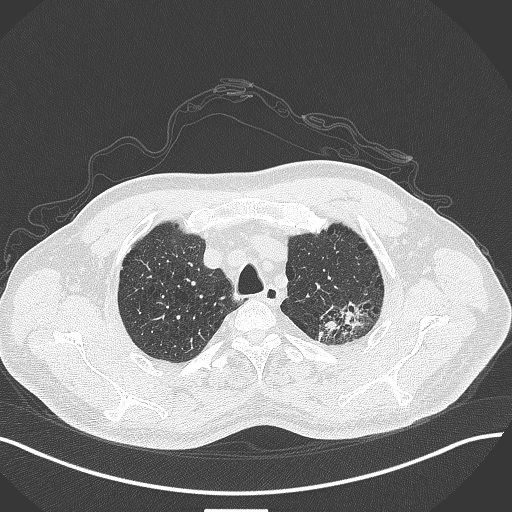
Chest CT, one axial slice. Position 356 of 429 along the scan axis. Reconstruction kernel B70f. 120 kVp. Lung window (W 1500 / L -600 HU). 1 mm slice thickness. 512 × 512 image matrix, field of view 400 × 400 mm. Male patient, age 55 years. From the clinical record (not read from this slice): clinical TNM (as recorded): T3 N0 M1c; histopathological grade: G3.
Outlined on this slice (rectangle marked by the reading radiologist):
- lung tumour (recorded histology: adenocarcinoma): bounding box <315,296,380,349> (left, top, right, bottom; pixels)